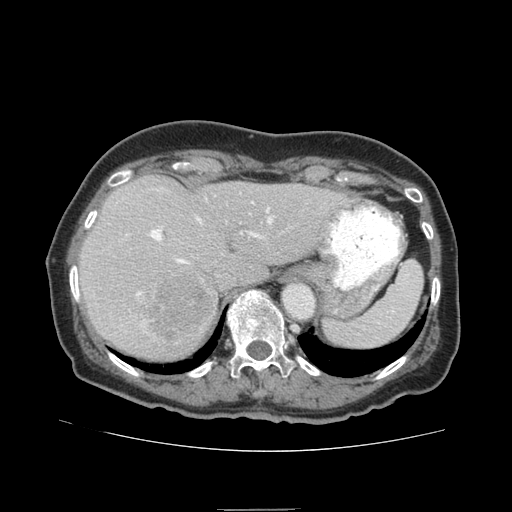
Contrast-enhanced abdominal CT (liver protocol), one axial slice; position 61 of 95 along the scan axis; reconstruction kernel STANDARD; soft-tissue window (W 400 / L 40 HU); 2.5 mm slice thickness; 512 × 512 image matrix, field of view 360 × 360 mm. Case-level facts recorded for this patient, not image findings: diagnosis: hepatocellular carcinoma (patient treated with transarterial chemoembolisation; whether this scan precedes or follows treatment is not stated here); TNM stage (as recorded): Stage-IVA; Child-Pugh class: B; tumour differentiation: moderately differentiated.
Annotated regions visible in this slice (semi-automatically segmented with operator editing):
- liver parenchyma outside the tumour (the mass and vessels are separate outlines, so this box may not span the whole liver): box from (x=78, y=176) to (x=351, y=360) px
- mass: (x=133, y=270)–(x=216, y=357)
- liver vessels: (x=136, y=202)–(x=273, y=296)